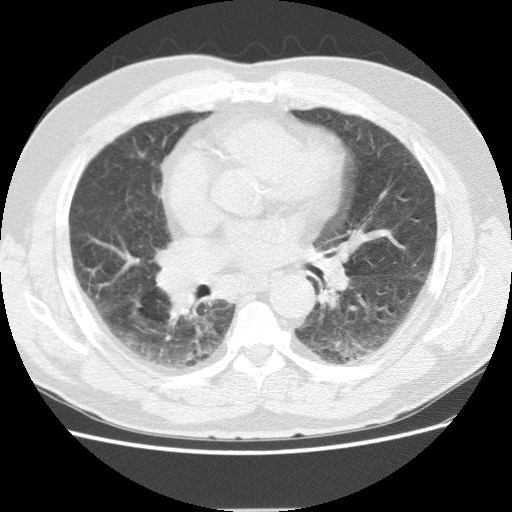
Low-dose screening chest CT, axial slice; baseline annual screen; lung window (W 1500 / L -600 HU); 120 kVp; 512 × 512 image matrix, field of view 361 × 361 mm. Male participant, aged 72 years at enrolment.
Lesion marked by an expert reader, bounding box [x1, y1, x2, y2] px = [149, 240, 194, 277]. Screening reader's record for this exam: no non-calcified nodule ≥4 mm recorded. Official screen result: negative screen, minor abnormalities not suspicious for lung cancer. Participant outcome: lung cancer diagnosed 163 days after this screen — adenocarcinoma, NOS, right middle lobe, stage IIIB (AJCC 6th edition), 27 mm at pathology.